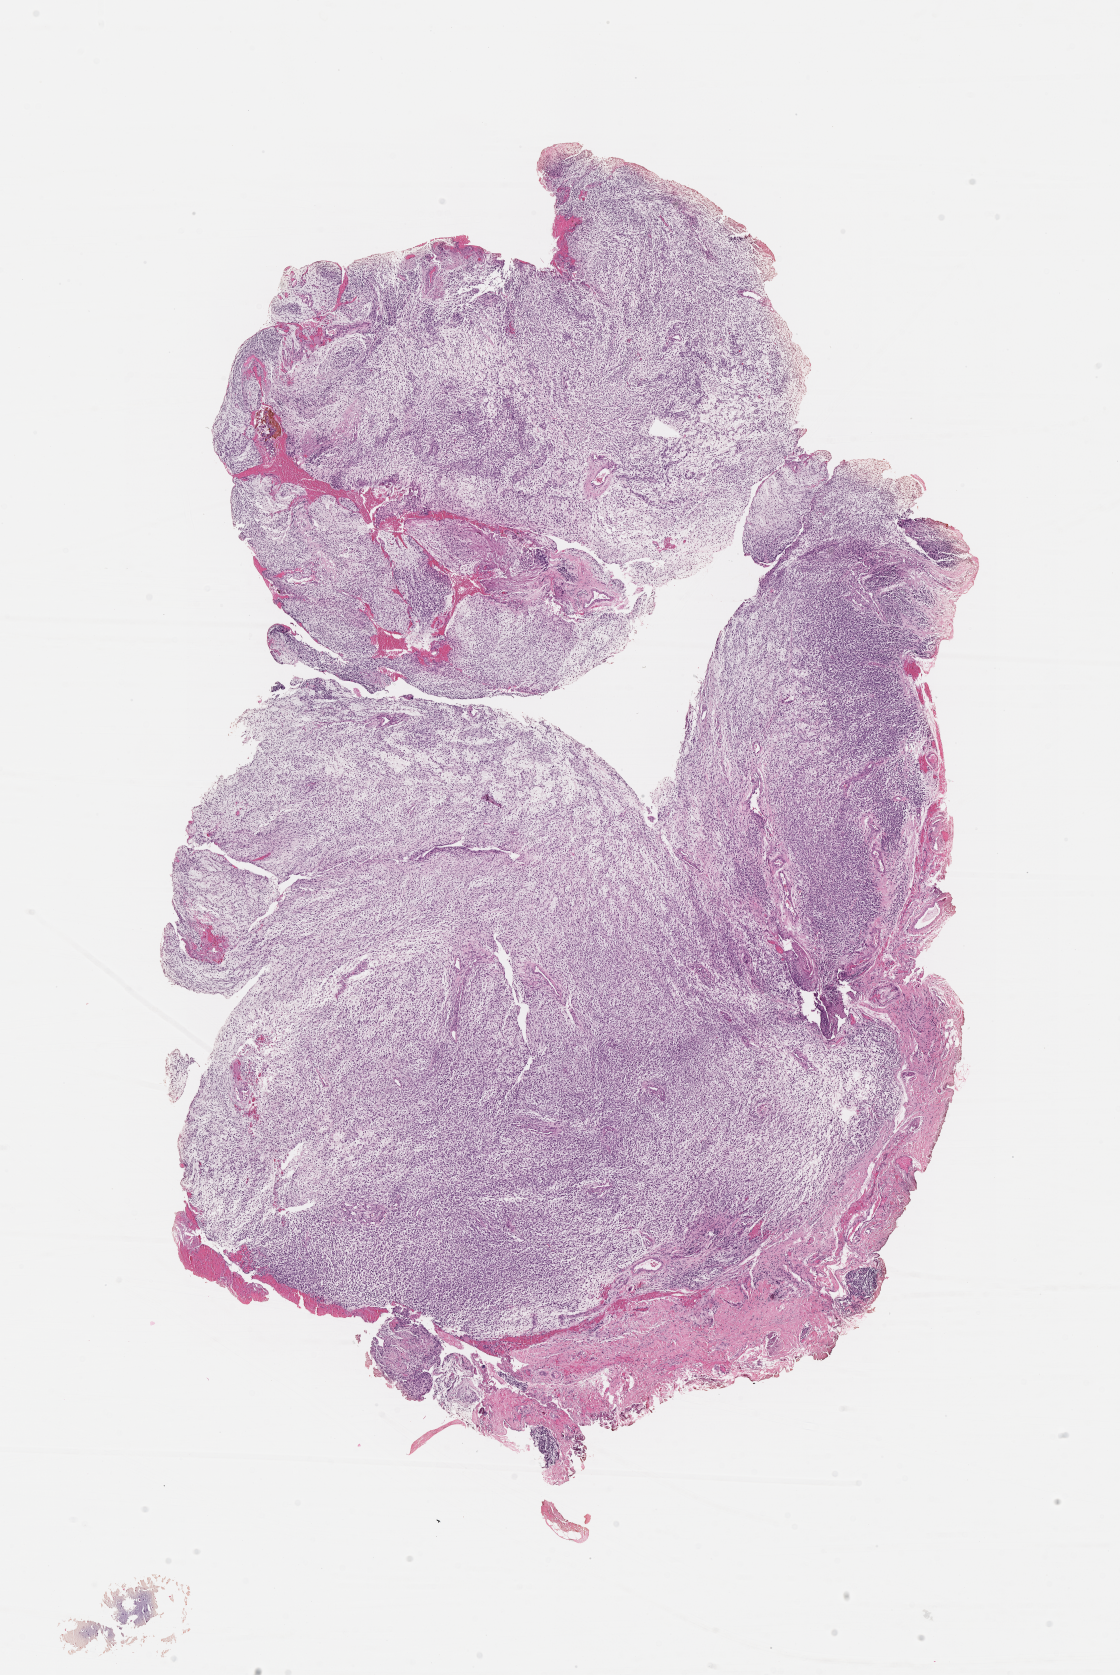
Whole-slide image, H&E stain of tumor tissue — whole scanned area (about 9.1 x 13.5 mm) shown as a low-resolution overview. Formalin-fixed paraffin-embedded section. Sample anatomic site: eye, orbit-right. Male patient, age at diagnosis 7.0 years.
Metastatic status at presentation (as recorded): non-metastatic (confirmed). Diagnosis: rhabdomyosarcoma; histological classification: embryonal rhabdomyosarcoma. Stage (as recorded): 1.